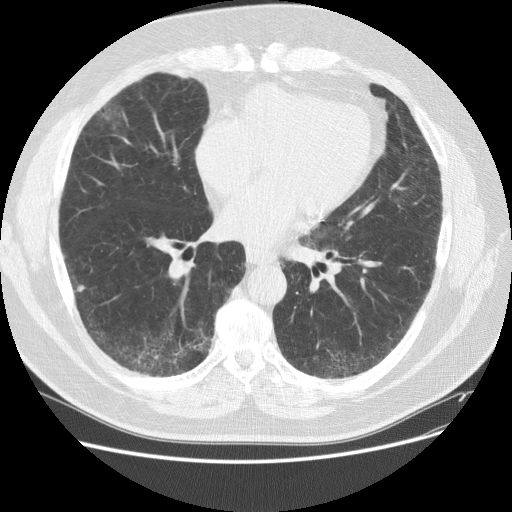
Axial slice from a low-dose chest CT screening exam. Baseline screening round. Lung window (W 1500 / L -600 HU). 2.5 mm slice thickness. Standard (soft-tissue) reconstruction kernel (STANDARD). 120 kVp. Slice 78 of 151 in the series. 512 × 512 image matrix. Male, age 59 years at enrolment. Current smoker at enrolment.
Lesion marked by an expert reader, bounding box [x1, y1, x2, y2] px = [84, 90, 131, 141]. The screening reader recorded 2 non-calcified nodules or masses ≥4 mm on this exam (right middle lobe, right lower lobe); which of them this box marks is not recorded.